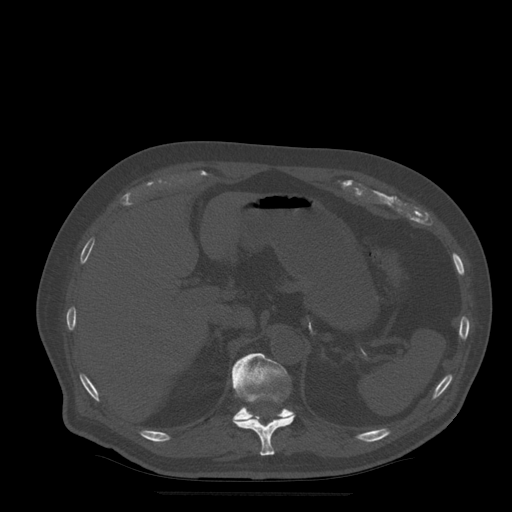
CT including the spine, one axial slice. Position 234 of 522 along the scan axis. Bone window (W 1800 / L 400 HU). 1.25 mm slice thickness. 512 × 512 image matrix, field of view 420 × 420 mm. Patient age 72 years. Case-level facts recorded for this patient, not image findings: primary cancer: prostate.
Annotated regions visible in this slice (semi-automatic segmentation, software-assisted and operator-edited):
- T11 vertebra: bounding box <233,414,296,456> (left, top, right, bottom; pixels)
- T12 vertebra: <232,353,294,420>